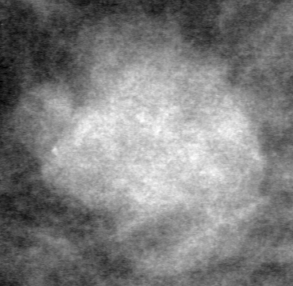
Region of interest cut from a scanned film mammogram (one marked finding), left breast, MLO view, BI-RADS breast density category 3 (scale 1–4).
Finding: mass, shape lobulated, margins circumscribed; BI-RADS assessment category 4; pathology (as recorded): malignant.